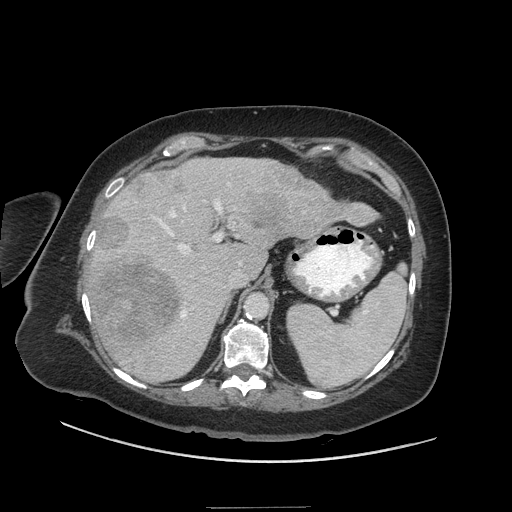
Contrast-enhanced abdominal CT (liver protocol), one axial slice; slice 35 of 81 in the series (ordered by position); reconstruction kernel STANDARD; 140 kVp; soft-tissue window (W 400 / L 40 HU); 2.5 mm slice thickness; 512 × 512 image matrix, field of view 440 × 440 mm. Case-level facts recorded for this patient, not image findings: diagnosis: hepatocellular carcinoma (patient treated with transarterial chemoembolisation; whether this scan precedes or follows treatment is not stated here); TNM stage (as recorded): Stage-II.
Structures marked on this image (semi-automatically segmented with operator editing):
- liver parenchyma outside the tumour (the mass and vessels are separate outlines, so this box may not span the whole liver): bounding box <90,158,363,382> (left, top, right, bottom; pixels)
- mass: <90,166,379,343>
- liver vessels: <119,171,254,328>